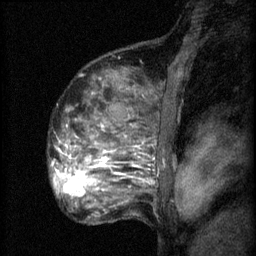
Breast MRI (dynamic contrast-enhanced), one sagittal slice. Slice 45 of 60 in the series (ordered by position). 3 images stored at this slice position (order not interpretable as contrast timing). 1.5 T. TE 4.2 ms, TR 8.2 ms. 2 mm slice thickness. 256 × 256 image matrix. Patient: female, 48 years.
Outlined on this slice (semi-automatically segmented with operator editing):
- analysis volume of interest (the breast-tissue region the enhancement analysis was run in; not a lesion): box from (x=61, y=138) to (x=153, y=201) px
- tumour enhancement mask (voxels above the 70 % enhancement threshold inside the analysis volume of interest): (x=61, y=160)–(x=104, y=197)